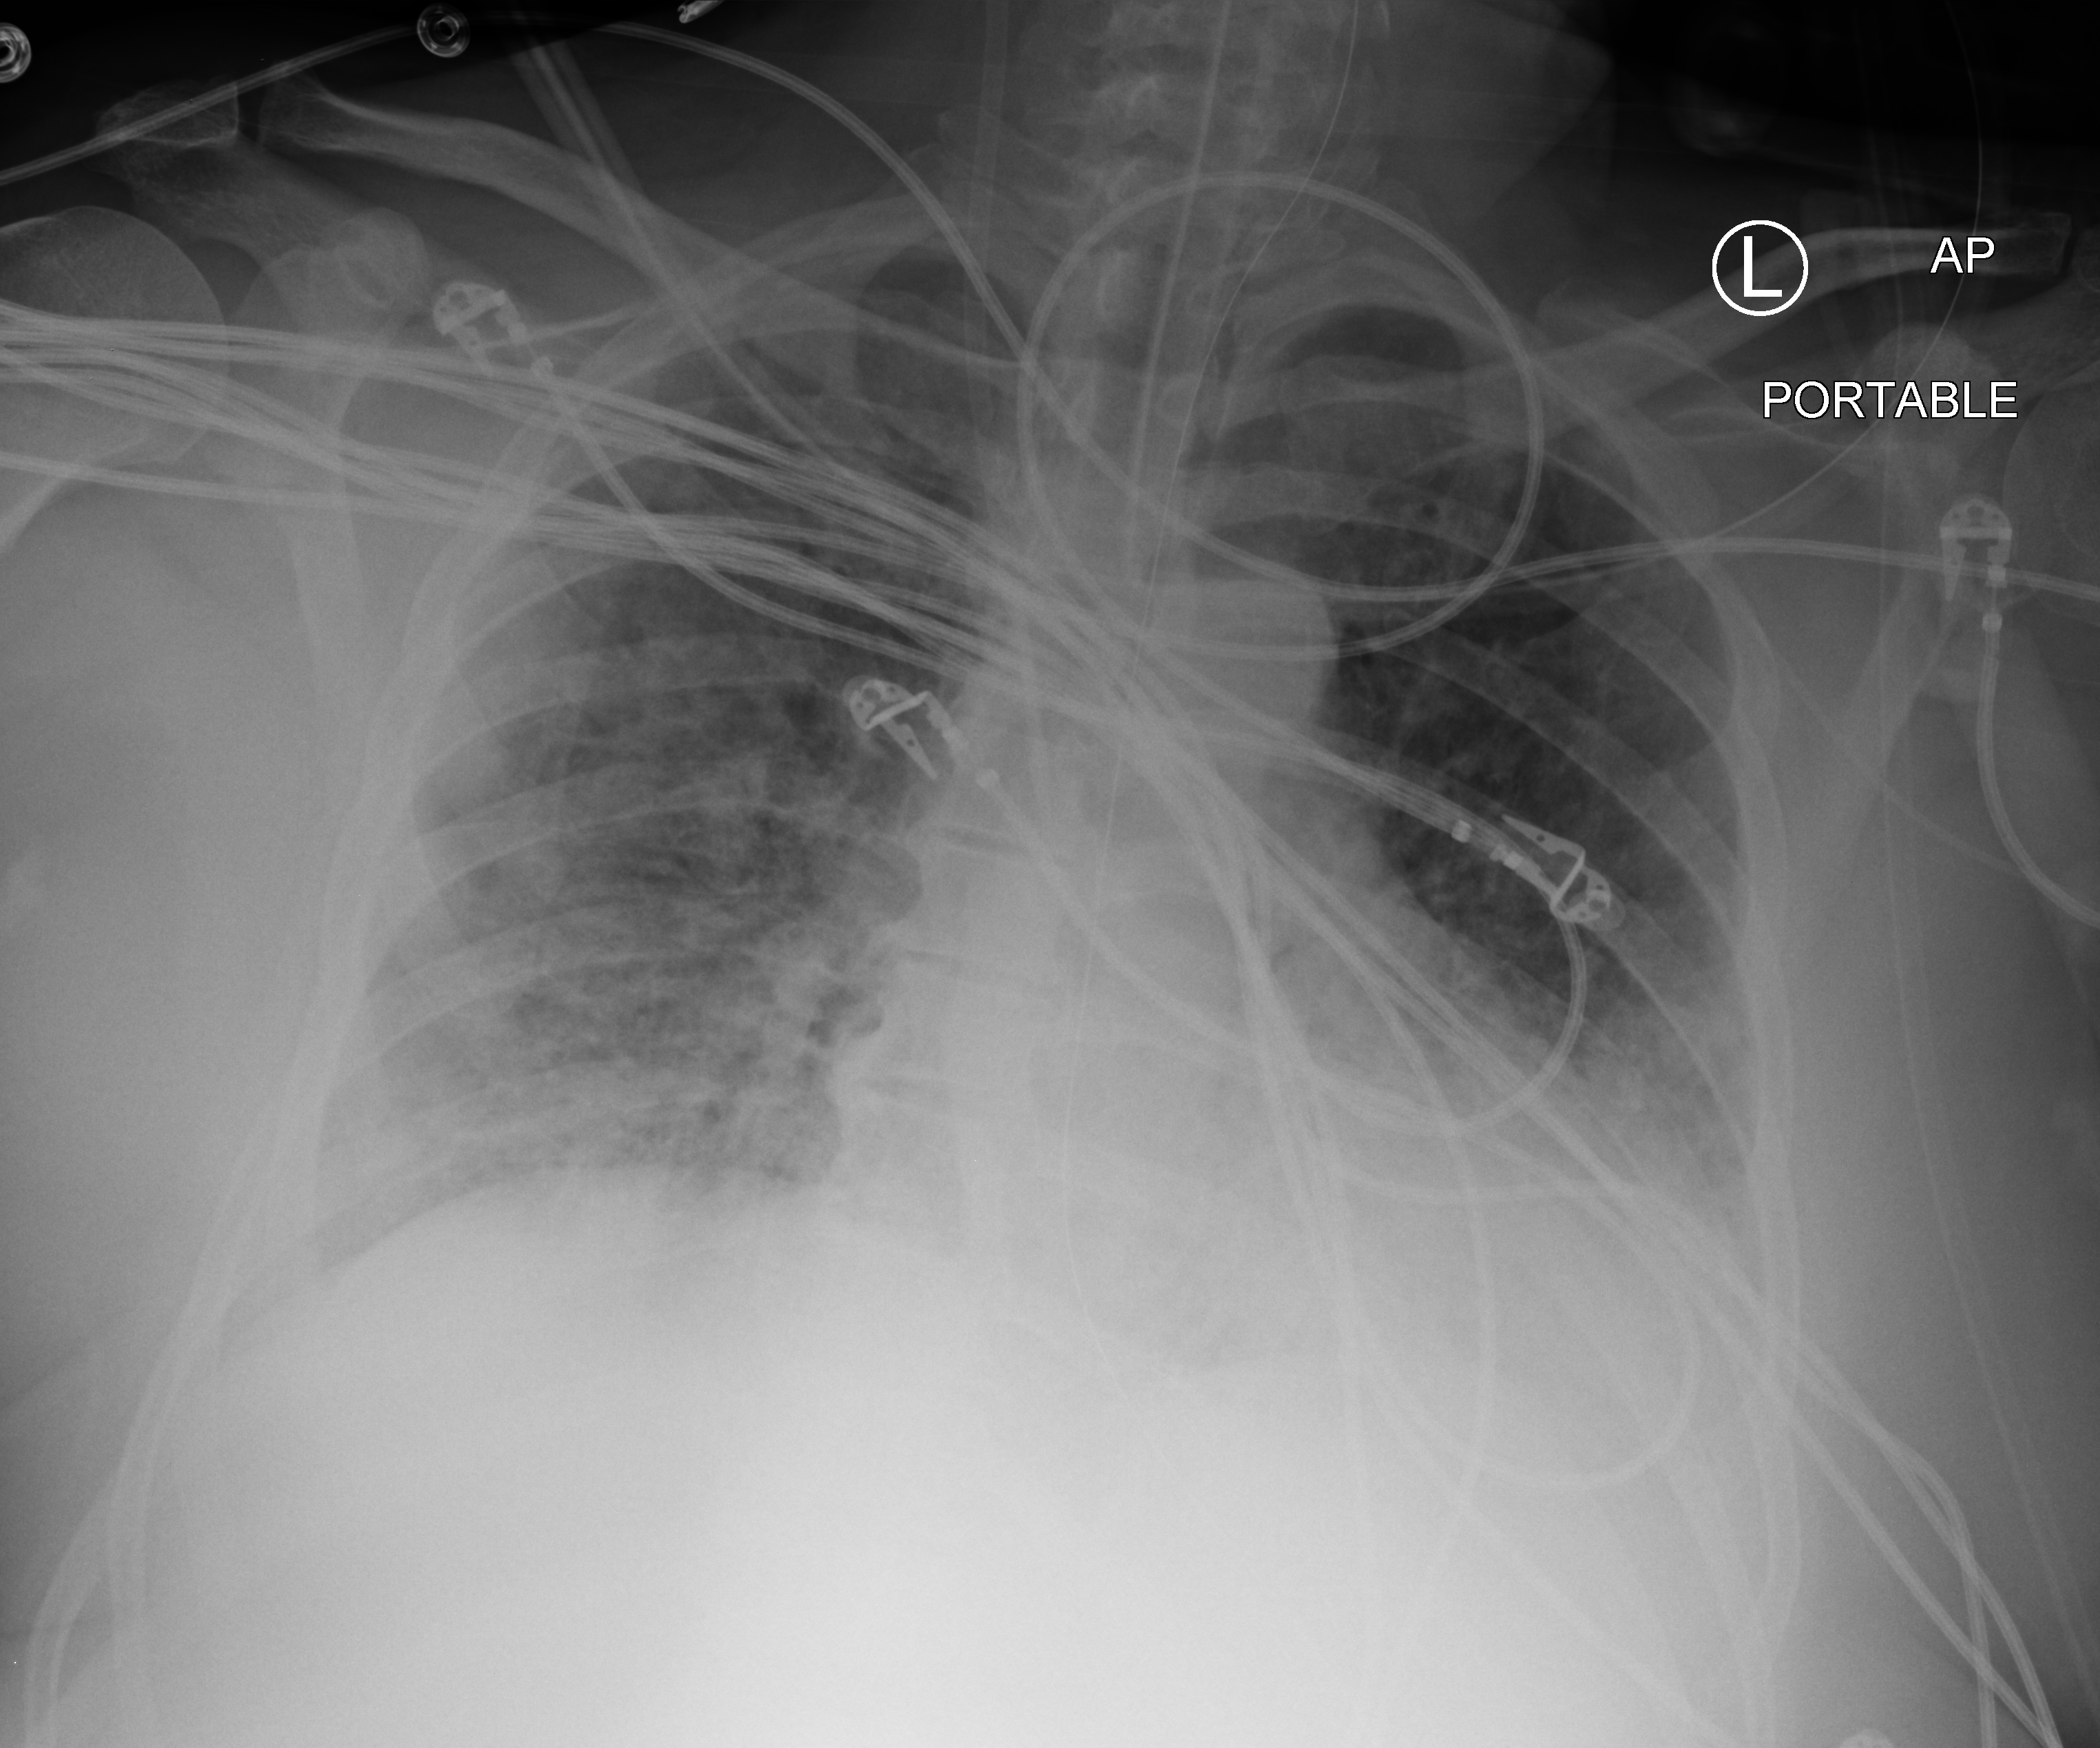
Chest X-ray (portable), anteroposterior (AP) projection. Patient hospitalised with COVID-19; male, aged 60–74 years.
Admission-level facts for this patient (not findings on this image; timing relative to this image not recorded): hypertension (admission record): yes; length of hospital stay: 40 days; COPD (admission record): no.